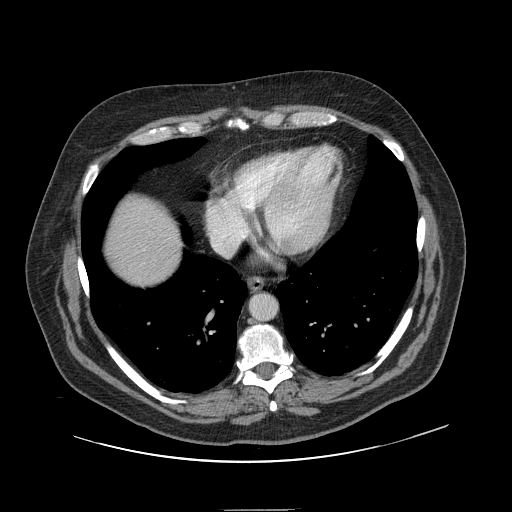
Contrast-enhanced abdominal CT, one axial slice; position 141 of 154 along the scan axis; intravenous contrast given; soft-tissue window (W 400 / L 40 HU); 2.5 mm slice thickness; 512 × 512 image matrix. Male patient, age 61 years. From the clinical record (not read from this slice): diagnosis: colorectal cancer liver metastases, imaged before liver resection; multiple liver metastases: yes; largest metastasis: 2.6 cm.
Outlined on this slice (expert manual segmentation):
- liver: box from (x=107, y=199) to (x=181, y=286) px
- planned liver remnant (the part of the liver to remain after resection): (x=107, y=198)–(x=181, y=286)